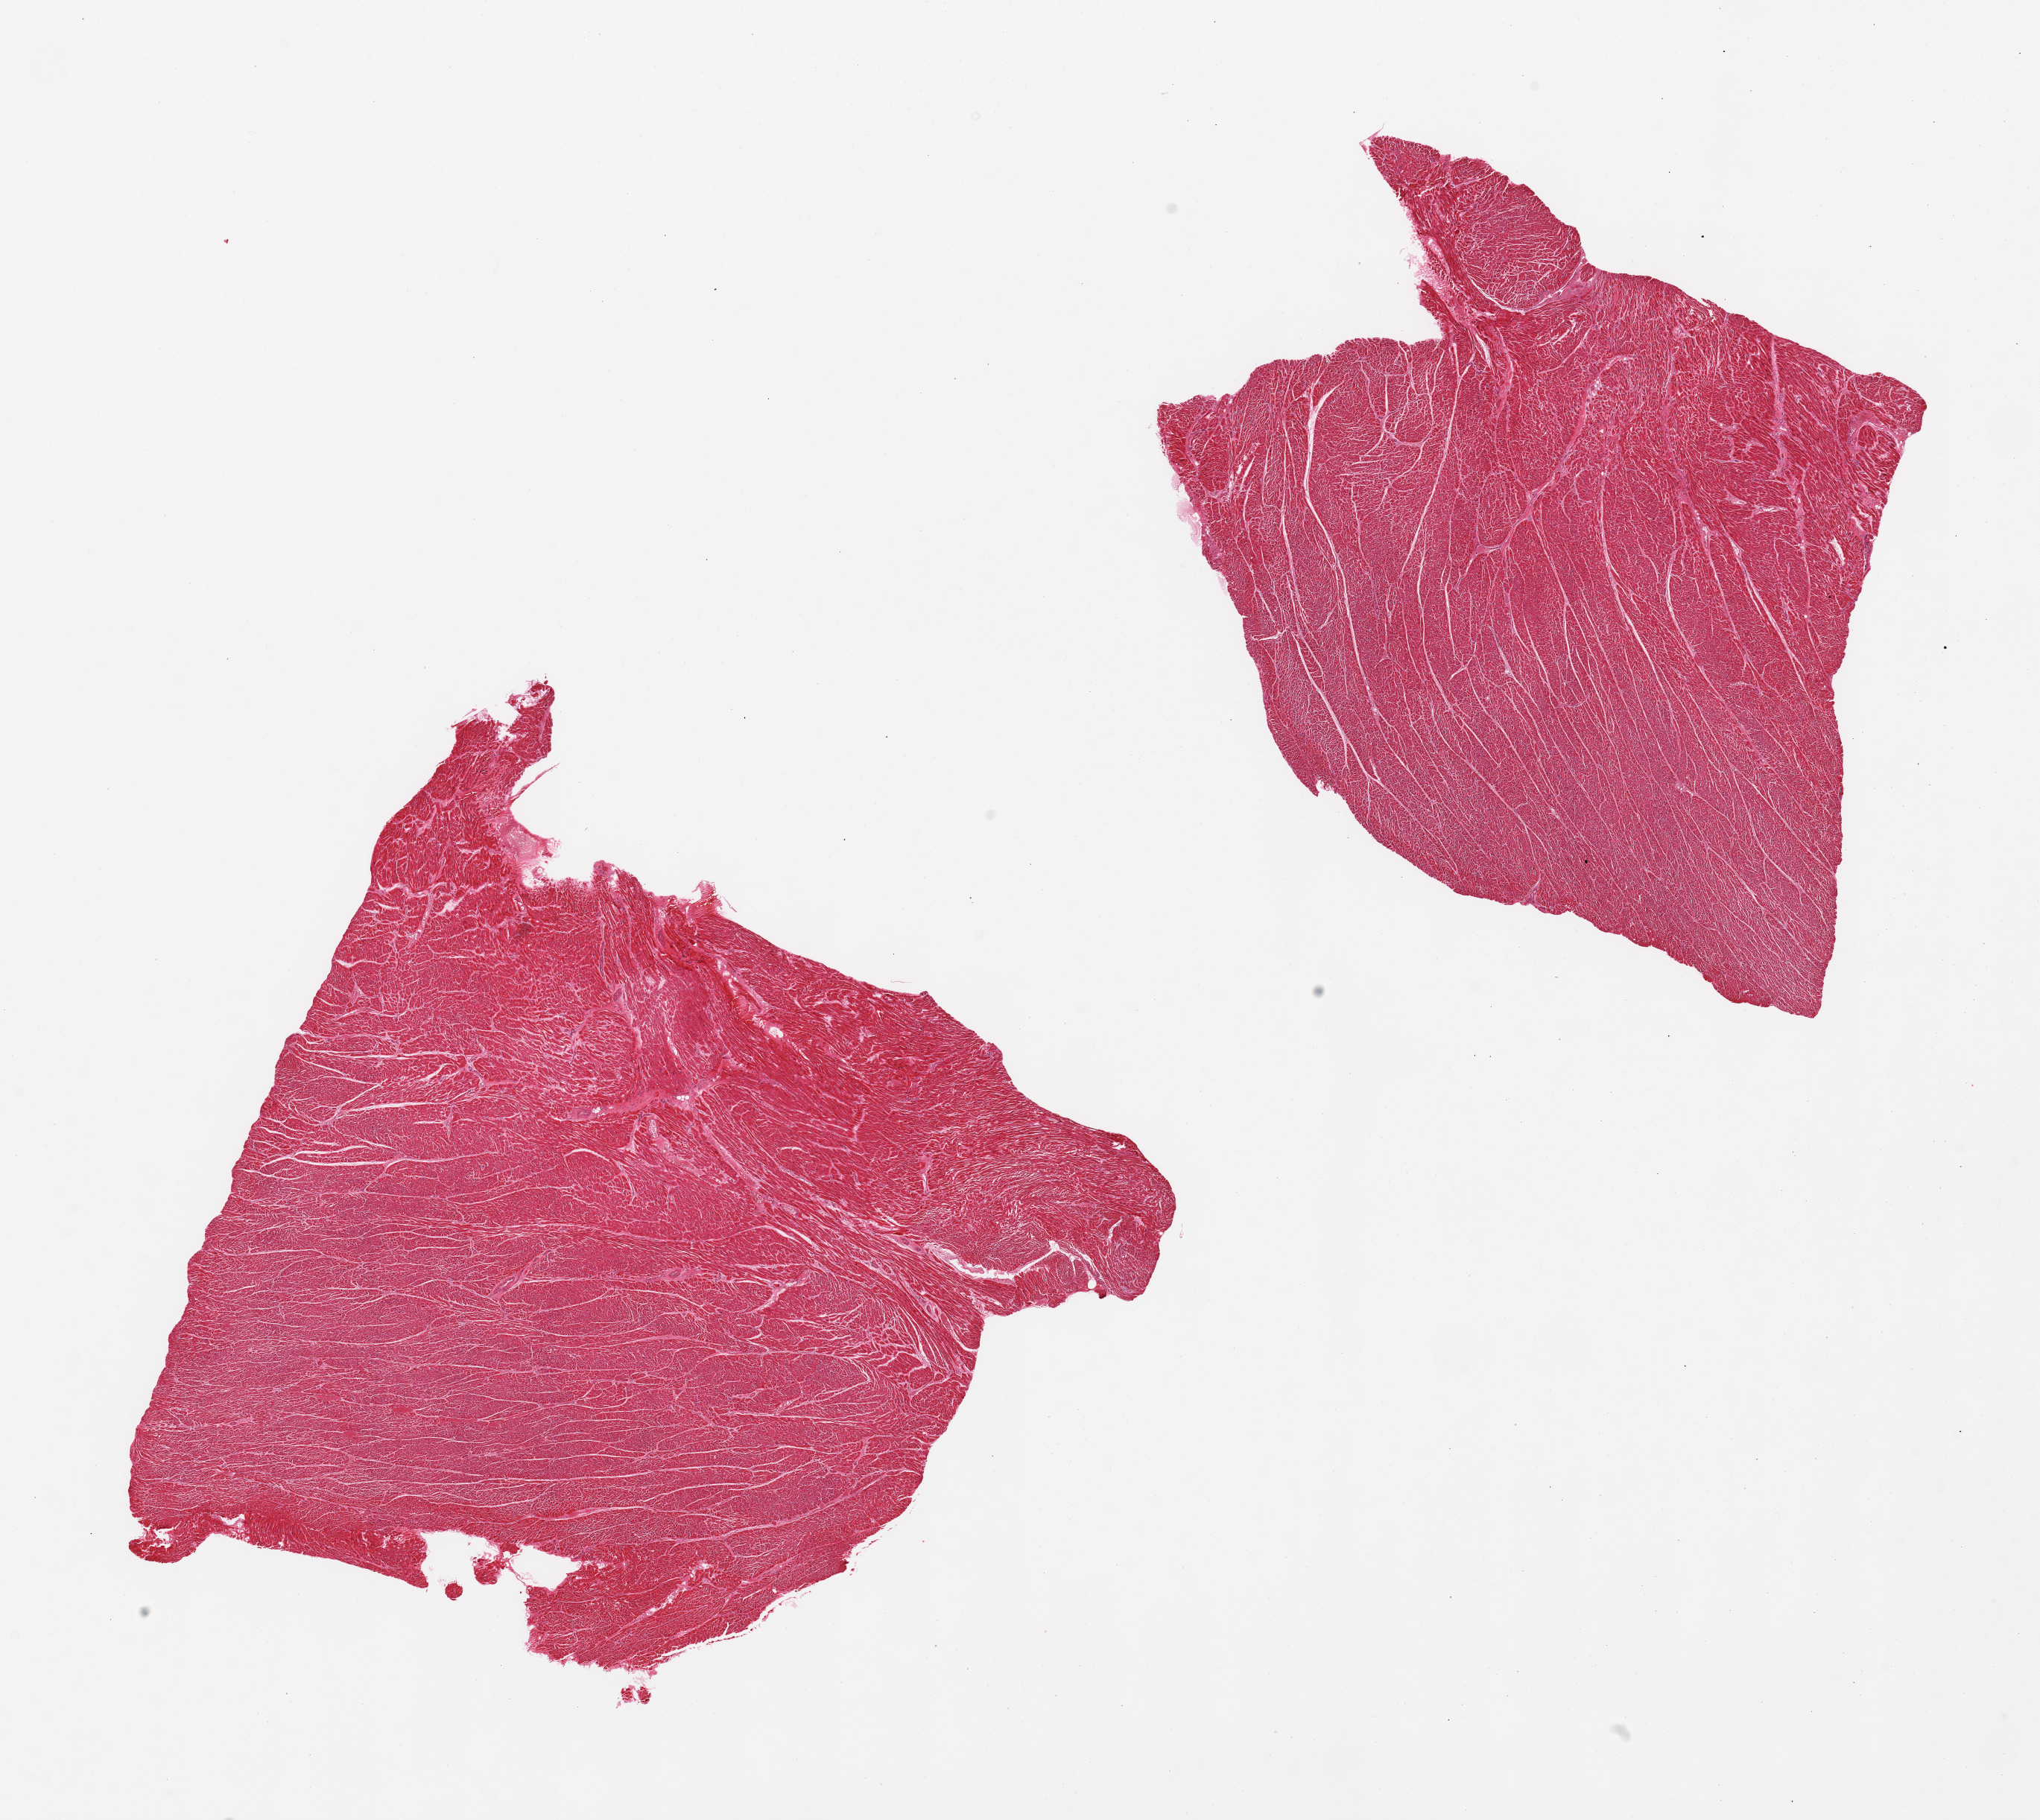
Digitized H&E-stained section, a low-resolution overview of the entire scanned area, about 21.7 x 19.3 mm (from a 20x scan), PAXgene-fixed, paraffin-embedded tissue, sampled site (target tissue): heart, tissue donor sample. Donor sex: male.
Pathologist's review note for this sample: 2 pieces, mild interstitial fibrosis, no infarcts noted.